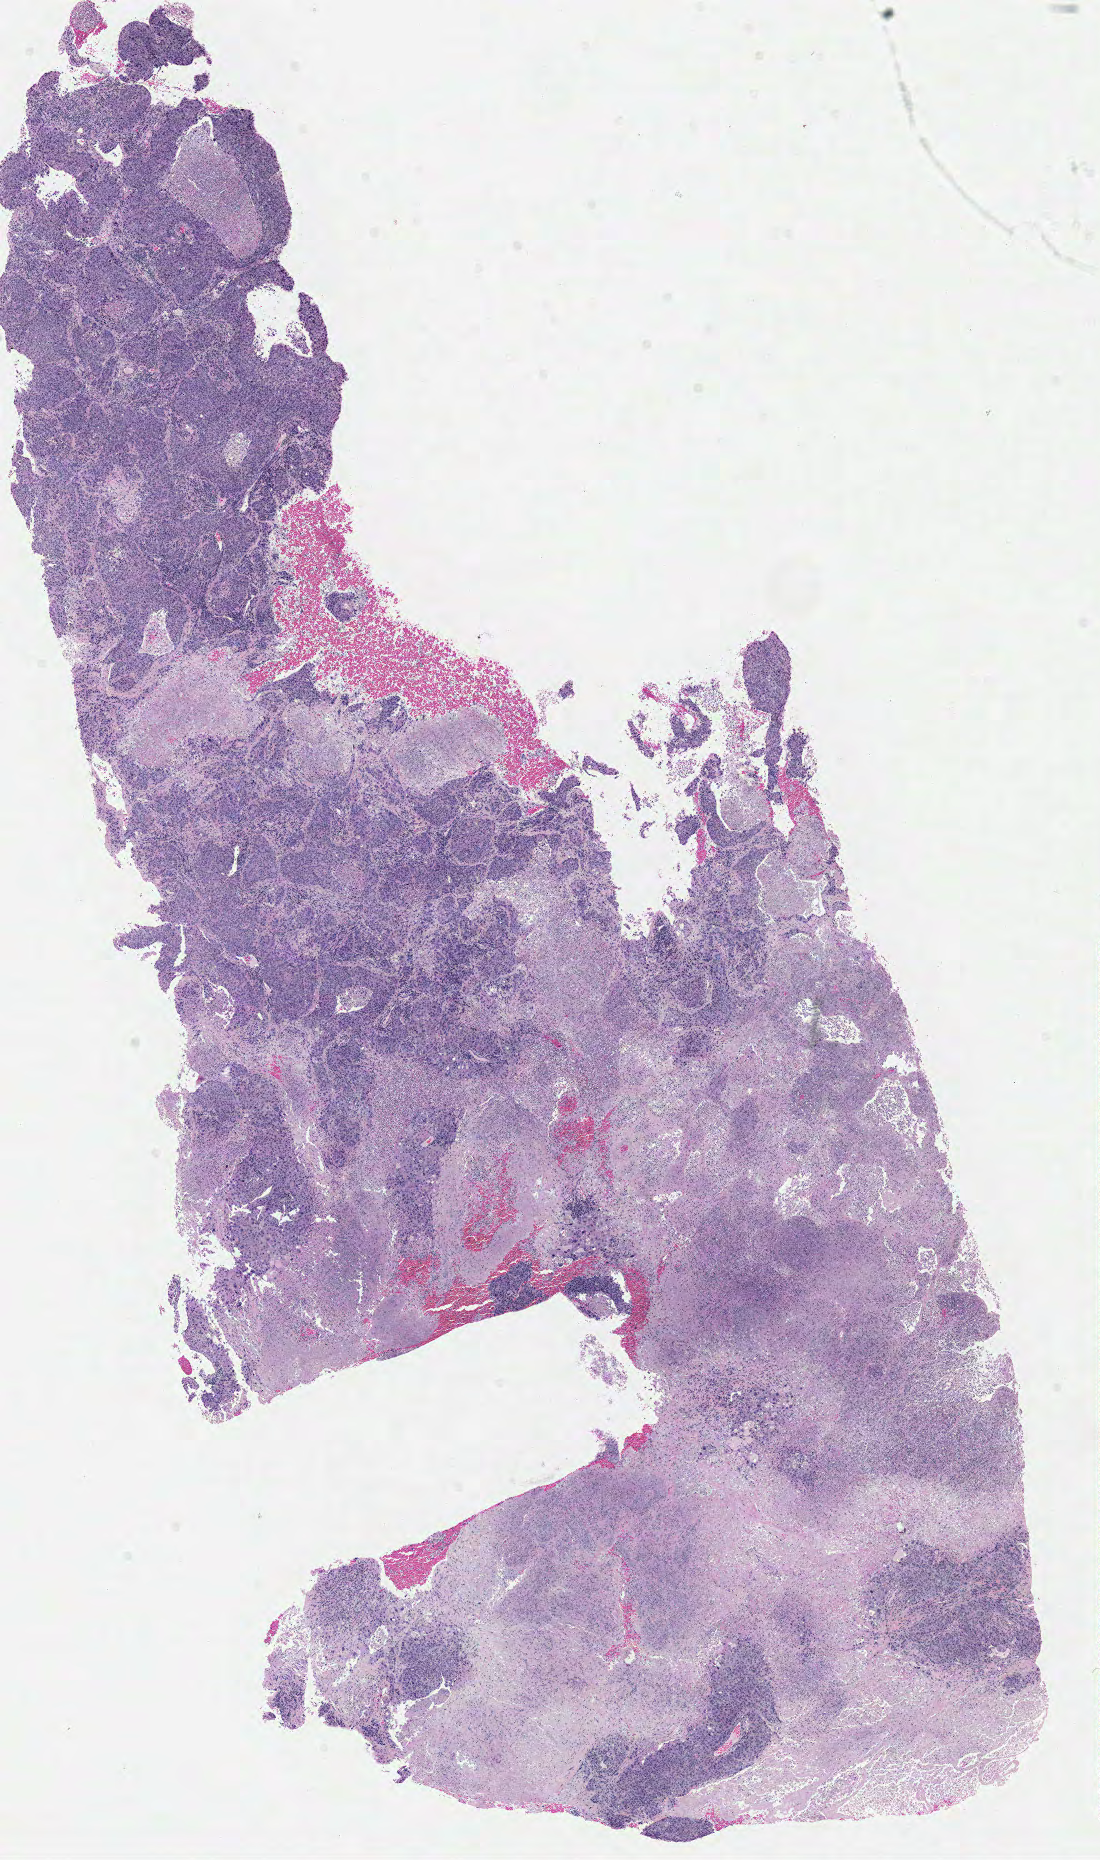
Digitized Hematoxylin and eosin (H&E) stained tissue section (whole slide), whole scanned area (about 8.7 x 14.7 mm, slide scanned at 40x) shown as a low-resolution overview; formalin-fixed paraffin-embedded (FFPE) diagnostic section; lung, primary tumour sample. Patient: male, age at initial diagnosis 65 years.
AJCC pathologic stage: IB (6th edition). Laterality: left. Diagnosis: Squamous cell carcinoma, NOS (upper lobe, lung).